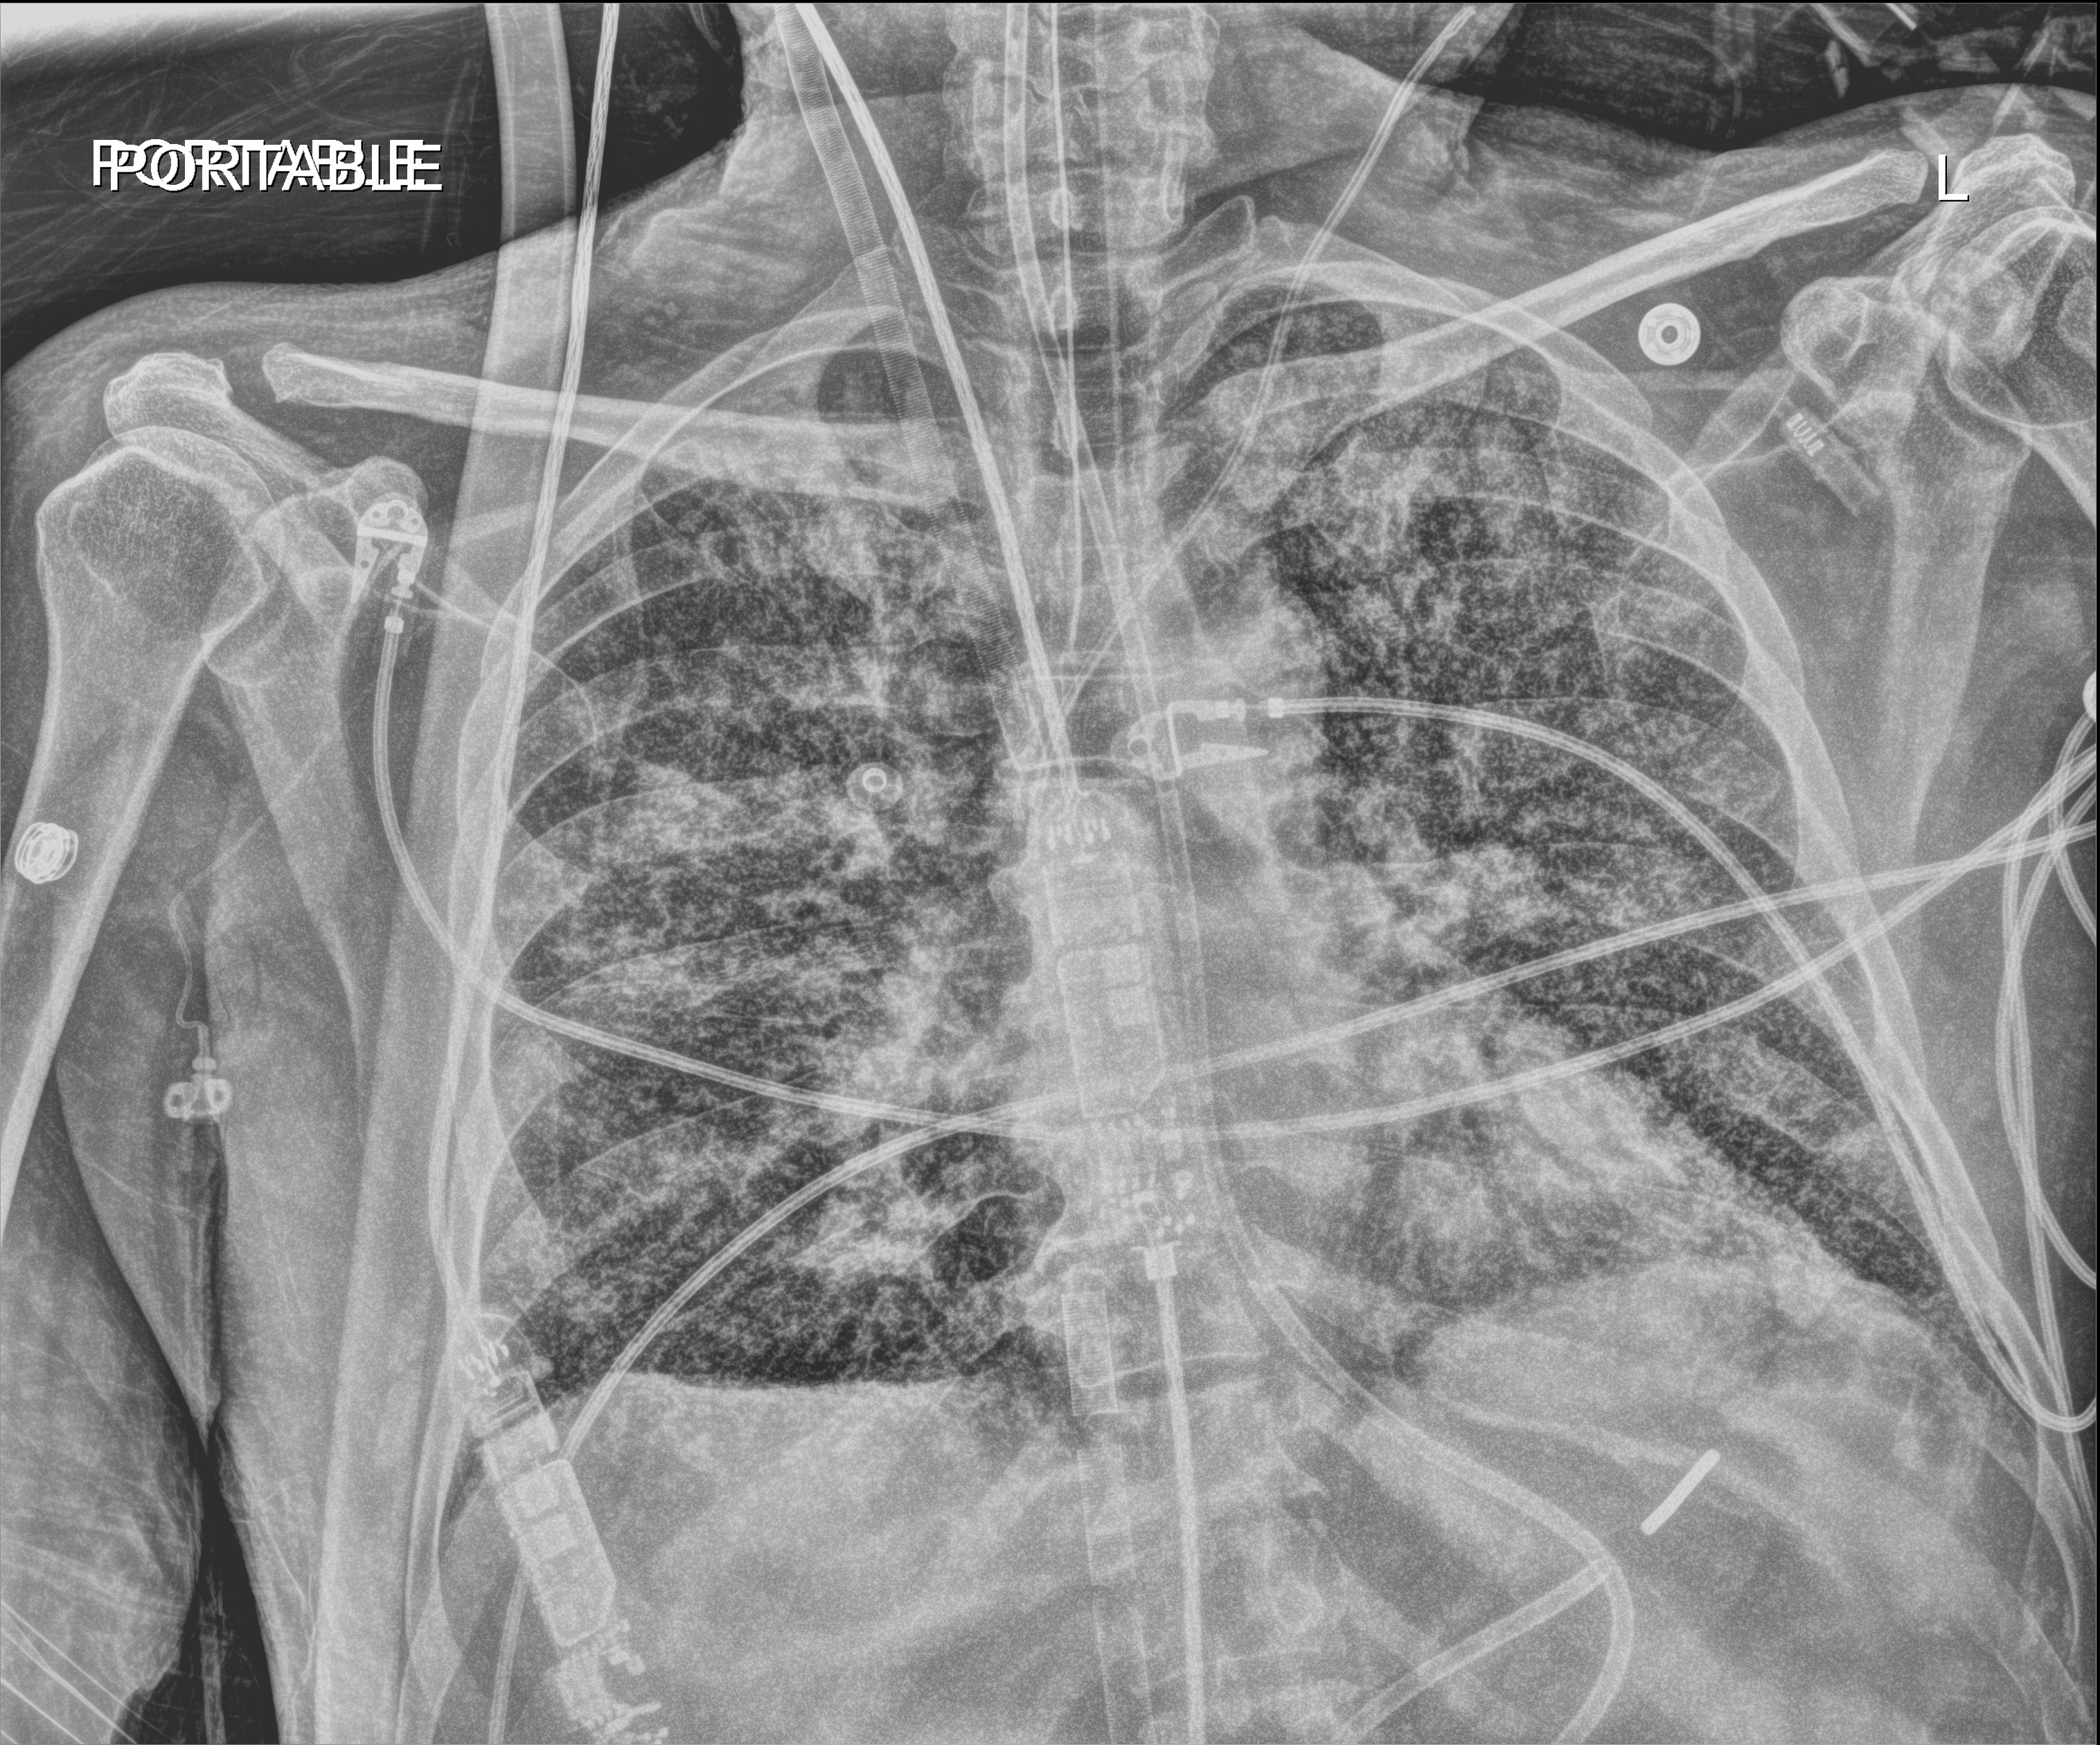
Bedside chest radiograph (digital radiography); anteroposterior (AP) projection. Male patient hospitalised with COVID-19, age 18–59 years.
Admission-level facts for this patient (not findings on this image; timing relative to this image not recorded): COPD (admission record): no.